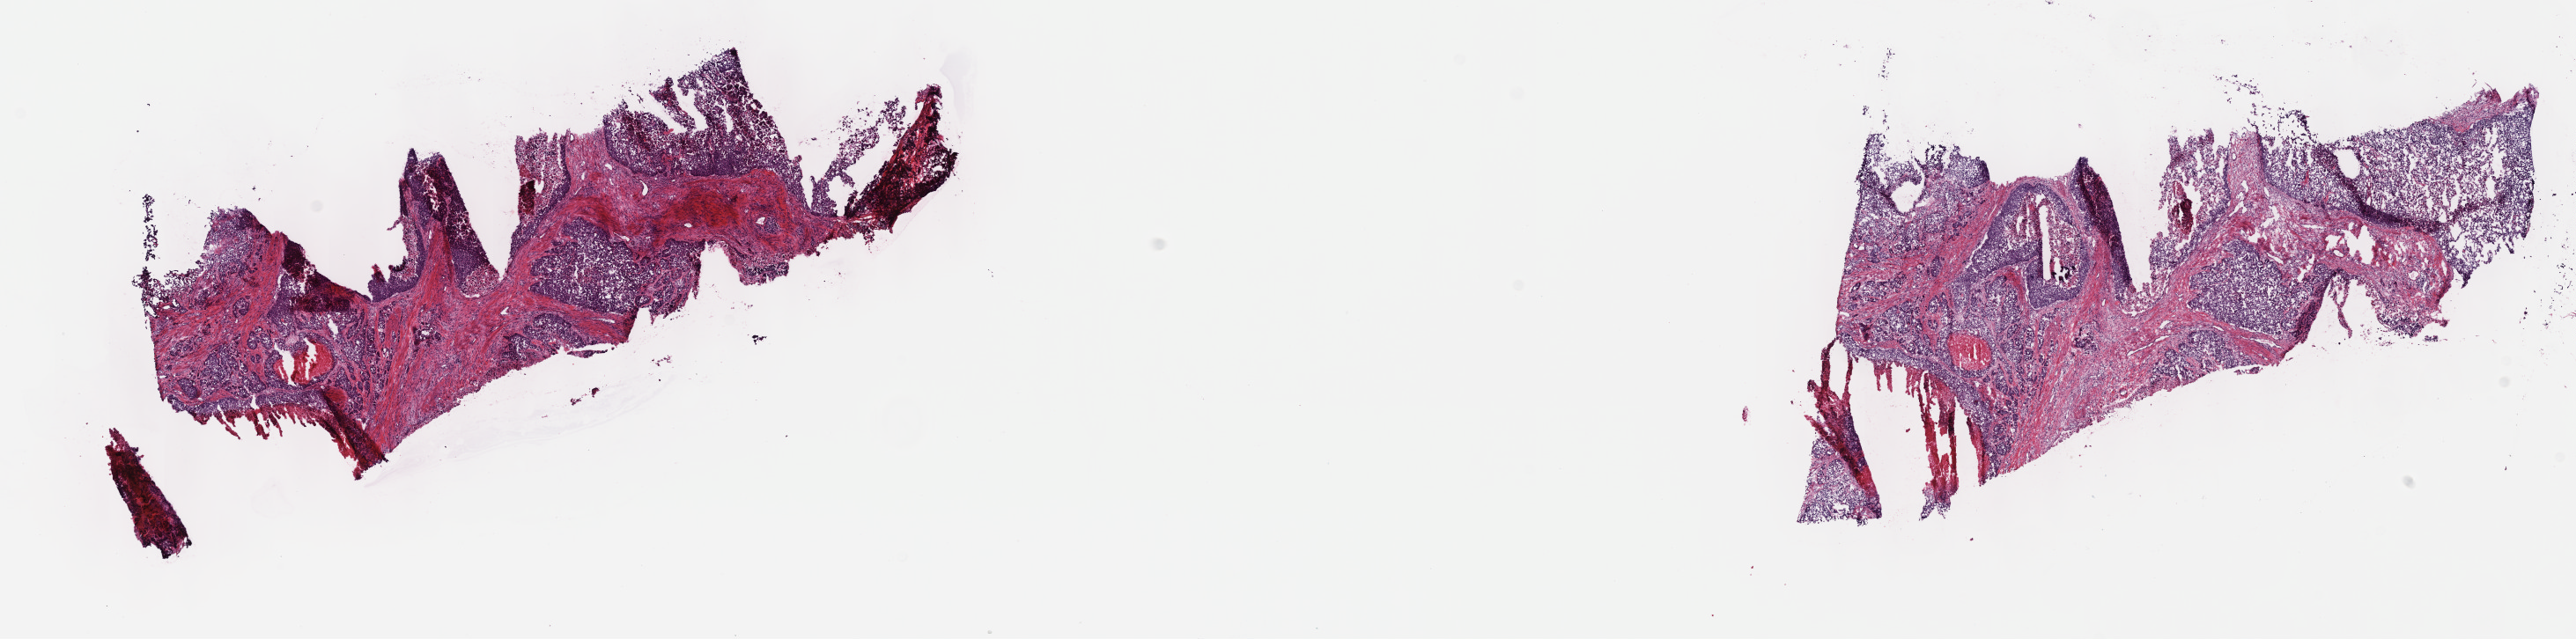
Hematoxylin and eosin (H&E) stained whole-slide image — a low-resolution overview of the entire scanned area, about 23.7 x 5.9 mm. Frozen section from the top of the tissue portion. Primary tumour sample from the bladder. Female patient; age at initial diagnosis 74 years. Histologic grade: high grade. Pathologist review of this section (percent, as recorded): tumour cells 70%, tumour nuclei 70%, normal cells 0%, stromal cells 23%, necrosis 7%. Infiltration values recorded for this section: lymphocyte infiltration 3%, monocyte infiltration 1%, neutrophil infiltration 5%.
AJCC pathologic stage: II (6th edition). Lymph nodes positive (case pathology): 0 of 24 examined. Histologic diagnosis: Transitional cell carcinoma.